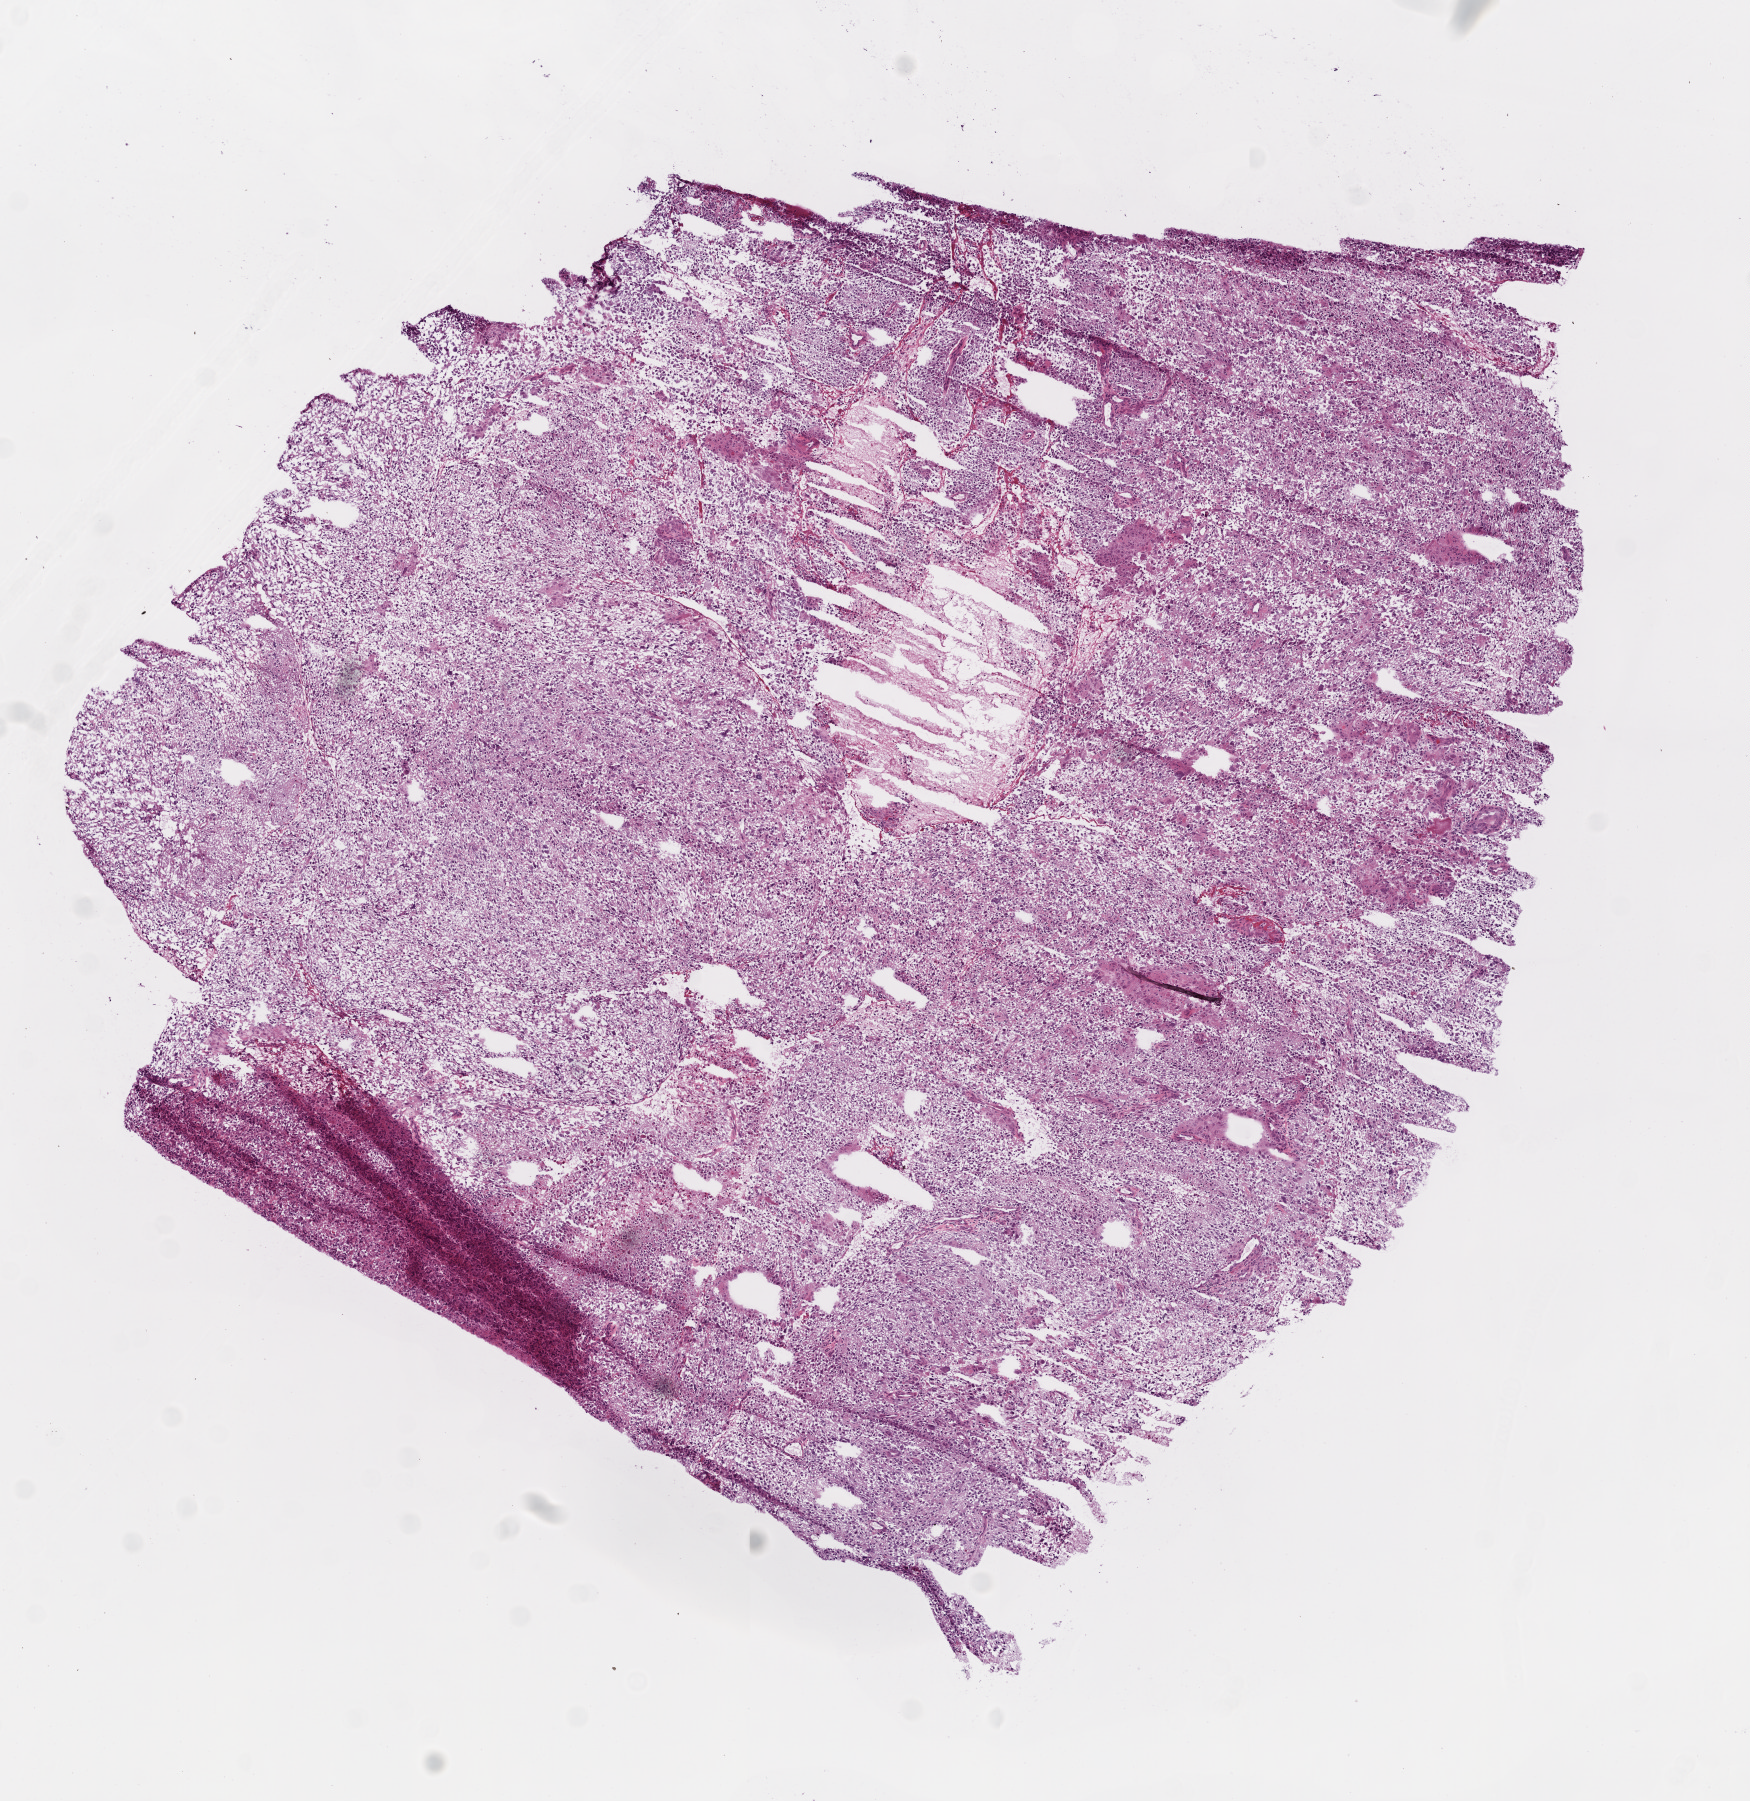
Digitized Hematoxylin and eosin (H&E) stained tissue section (whole slide), whole scanned area (about 7.0 x 7.2 mm, slide scanned at 20x) shown as a low-resolution overview; frozen section; brain, primary tumour sample. Patient: male, age at initial diagnosis 40 years. Composition of this section per pathologist review: tumour cells 99%, tumour nuclei 85%, normal cells 0%, stromal cells 0%, necrosis 1%.
Diagnosis: Glioblastoma.